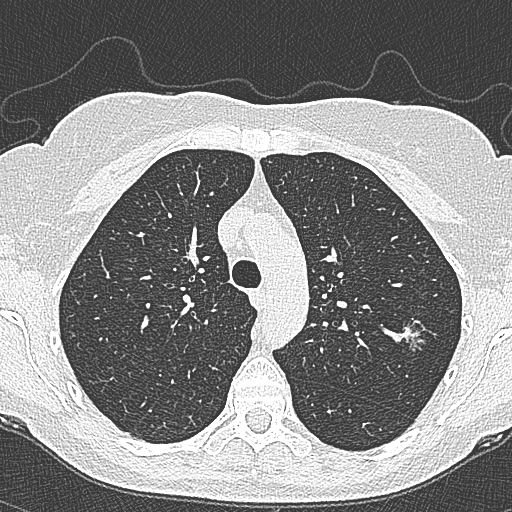
Low-dose screening chest CT, axial slice. Second screening round (one year after baseline). Lung window (W 1500 / L -600 HU). 120 kVp. Female participant, aged 65 years at enrolment. Current smoker at enrolment.
Expert reader's lesion annotation, bounding box [x1, y1, x2, y2] px = [392, 309, 438, 355]. The screening reader recorded 4 non-calcified nodules or masses ≥4 mm on this exam; which of them this box marks is not recorded. Official screen result: positive, change unspecified: nodule(s) >= 4 mm or enlarging nodule(s), mass(es), or other non-specific abnormalities suspicious for lung cancer. Later outcome: lung cancer diagnosed 54 days after this screen — bronchiolo-alveolar carcinoma, non-mucinous, left upper lobe, stage IA (AJCC 6th edition), 10 mm at pathology.